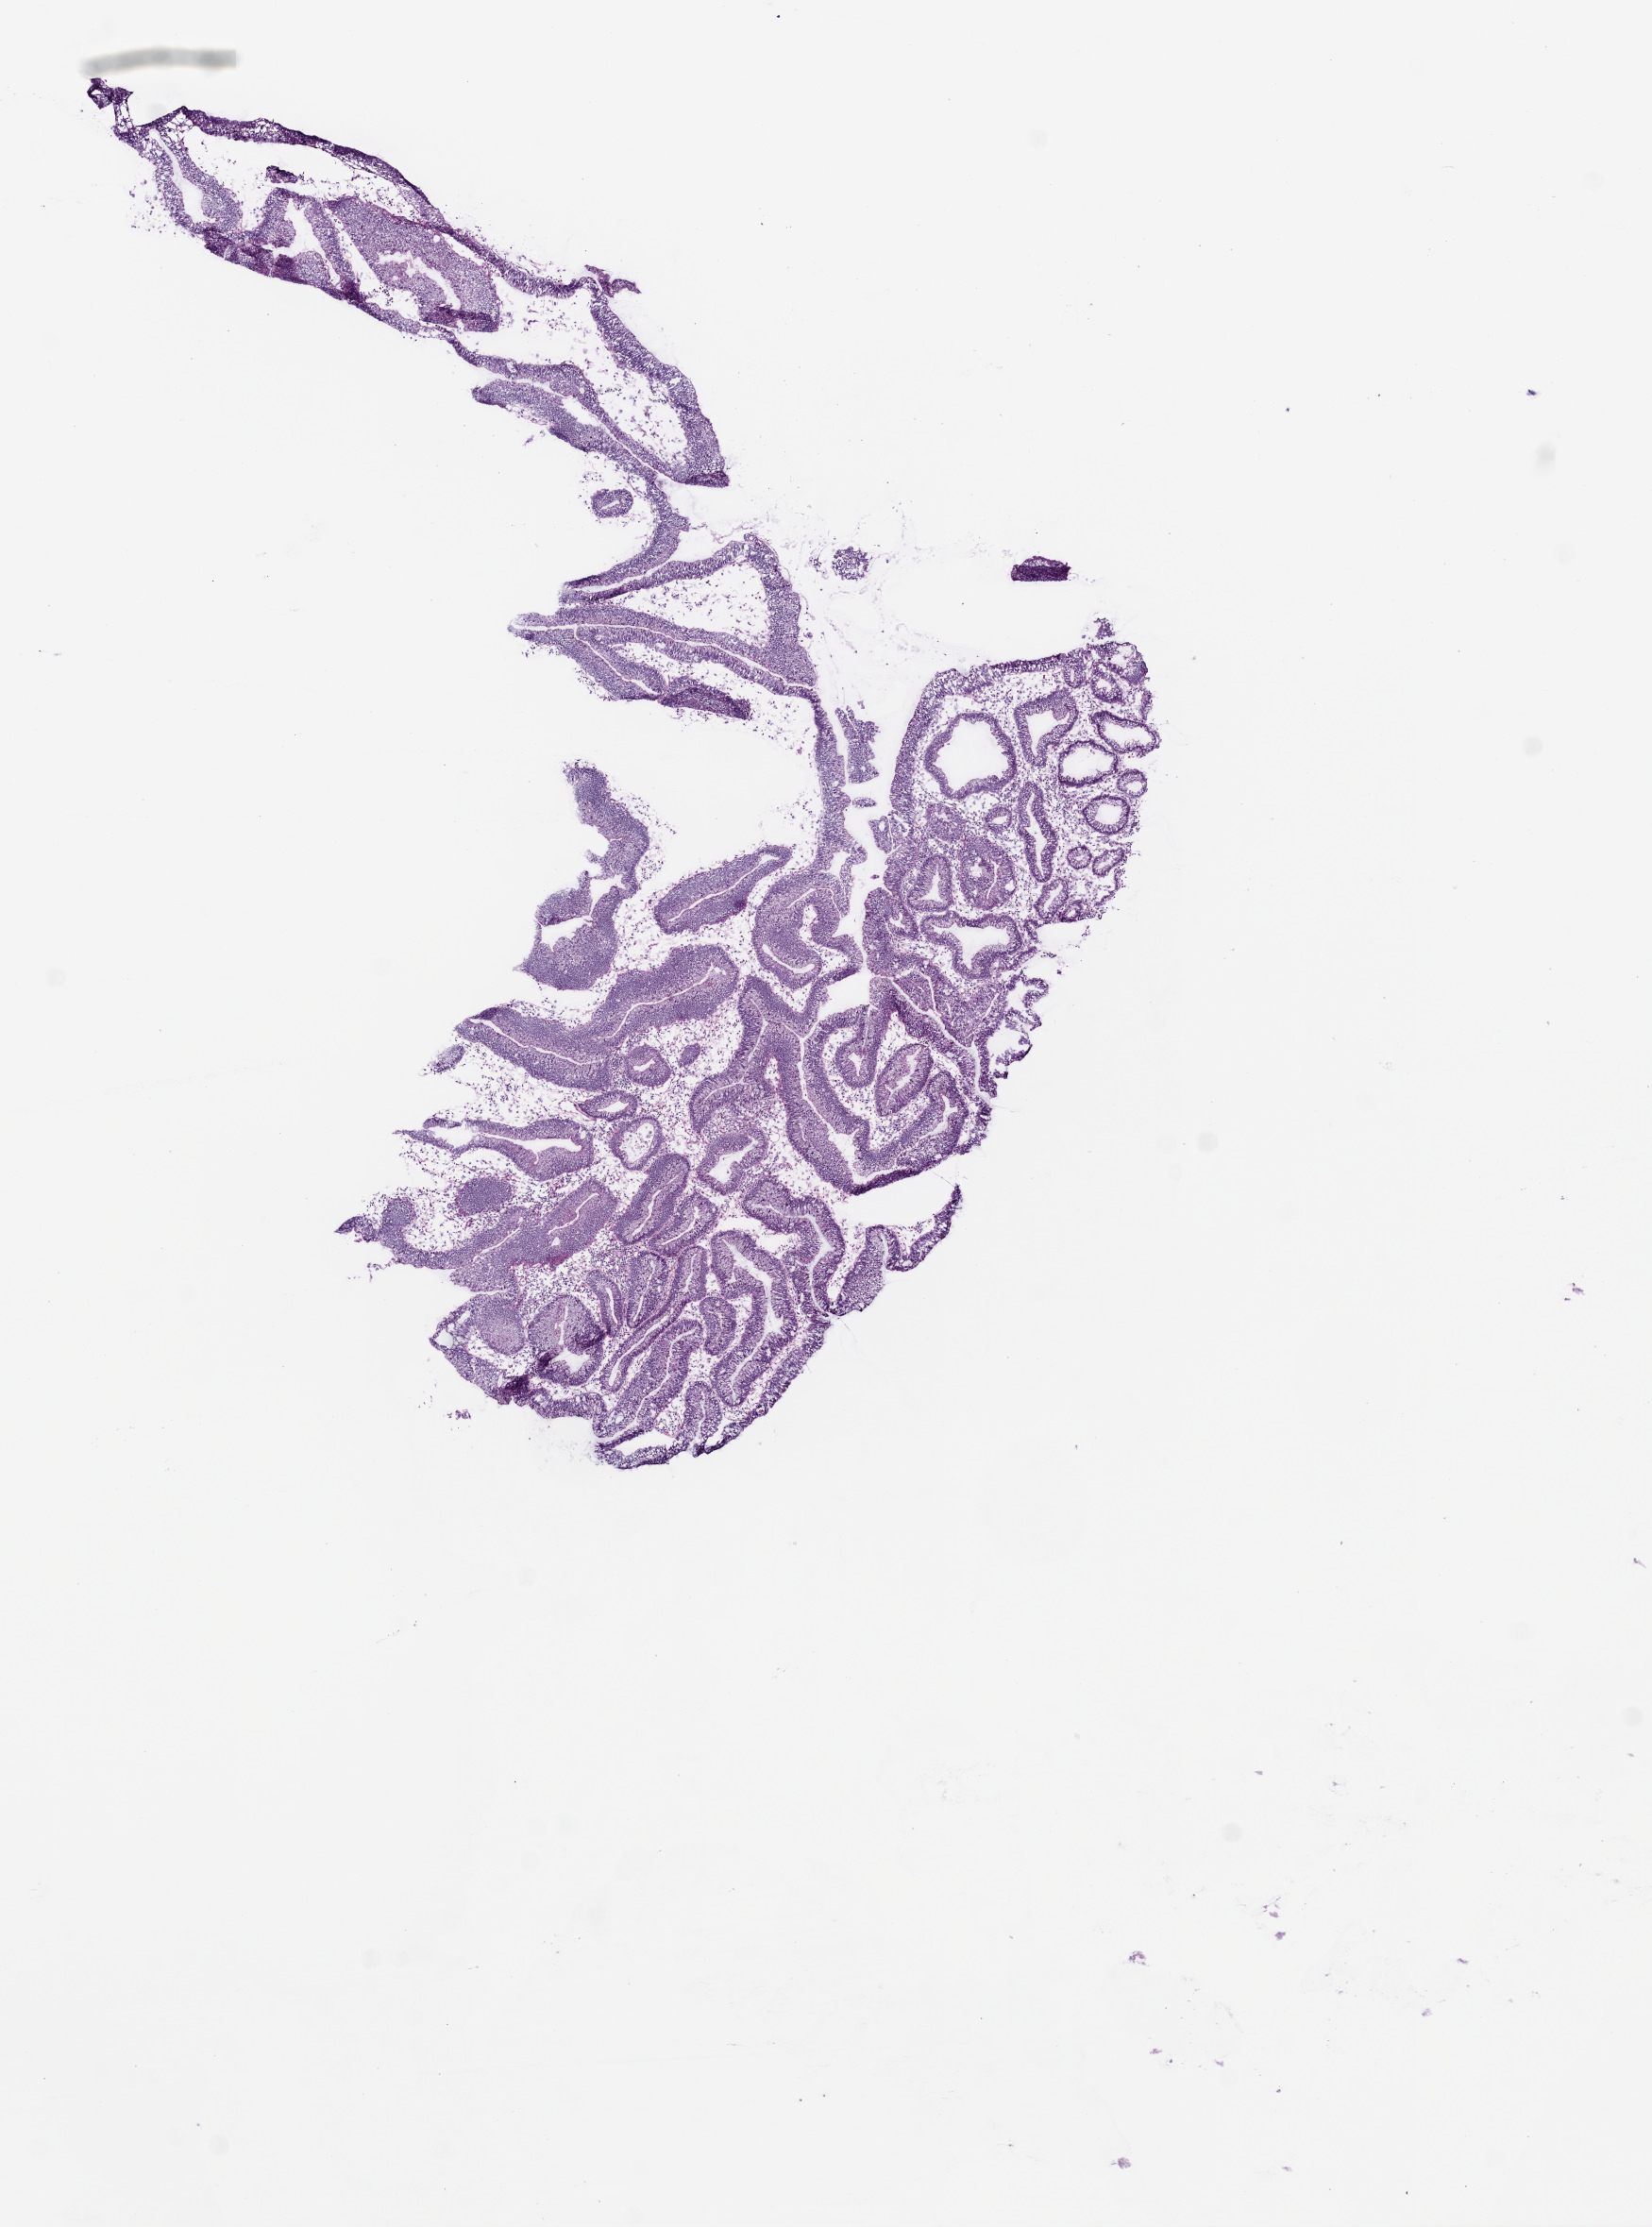
Whole-slide histology image, H&E, whole scanned area (about 7.0 x 9.5 mm, from a 20x scan) shown as a low-resolution overview, frozen section from the bottom of the tissue portion, primary tumour sample from the rectum. Female, age 78 years at initial diagnosis. Pathologist review of this section (percent, as recorded): tumour cells 90%, tumour nuclei 75%, normal cells 0%, stromal cells 10%, necrosis 0%.
- lymph nodes positive (case pathology): 0 of 12 examined
- histologic diagnosis: Adenocarcinoma, NOS (rectosigmoid junction)
- AJCC pathologic stage: I (5th edition)